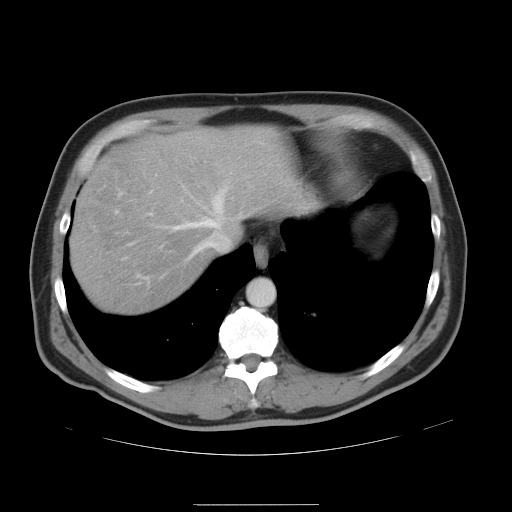
Contrast-enhanced abdominal CT, one axial slice. Position 40 of 47 along the scan axis. 120 kVp. Intravenous contrast given. Soft-tissue window (W 400 / L 40 HU). 5 mm slice thickness. 512 × 512 image matrix, field of view 420 × 420 mm. Male patient, age 61 years. Case-level facts recorded for this patient, not image findings: diagnosis: colorectal cancer liver metastases, imaged before liver resection; multiple liver metastases: no; largest metastasis: 1.2 cm; disease in both lobes: no.
Structures marked on this image (outlined manually by an expert reader):
- hepatic veins: bounding box (x1, y1, x2, y2) in pixels: (151, 189, 241, 257)
- liver: (70, 126, 296, 315)
- planned liver remnant (the part of the liver to remain after resection): (70, 125, 296, 315)